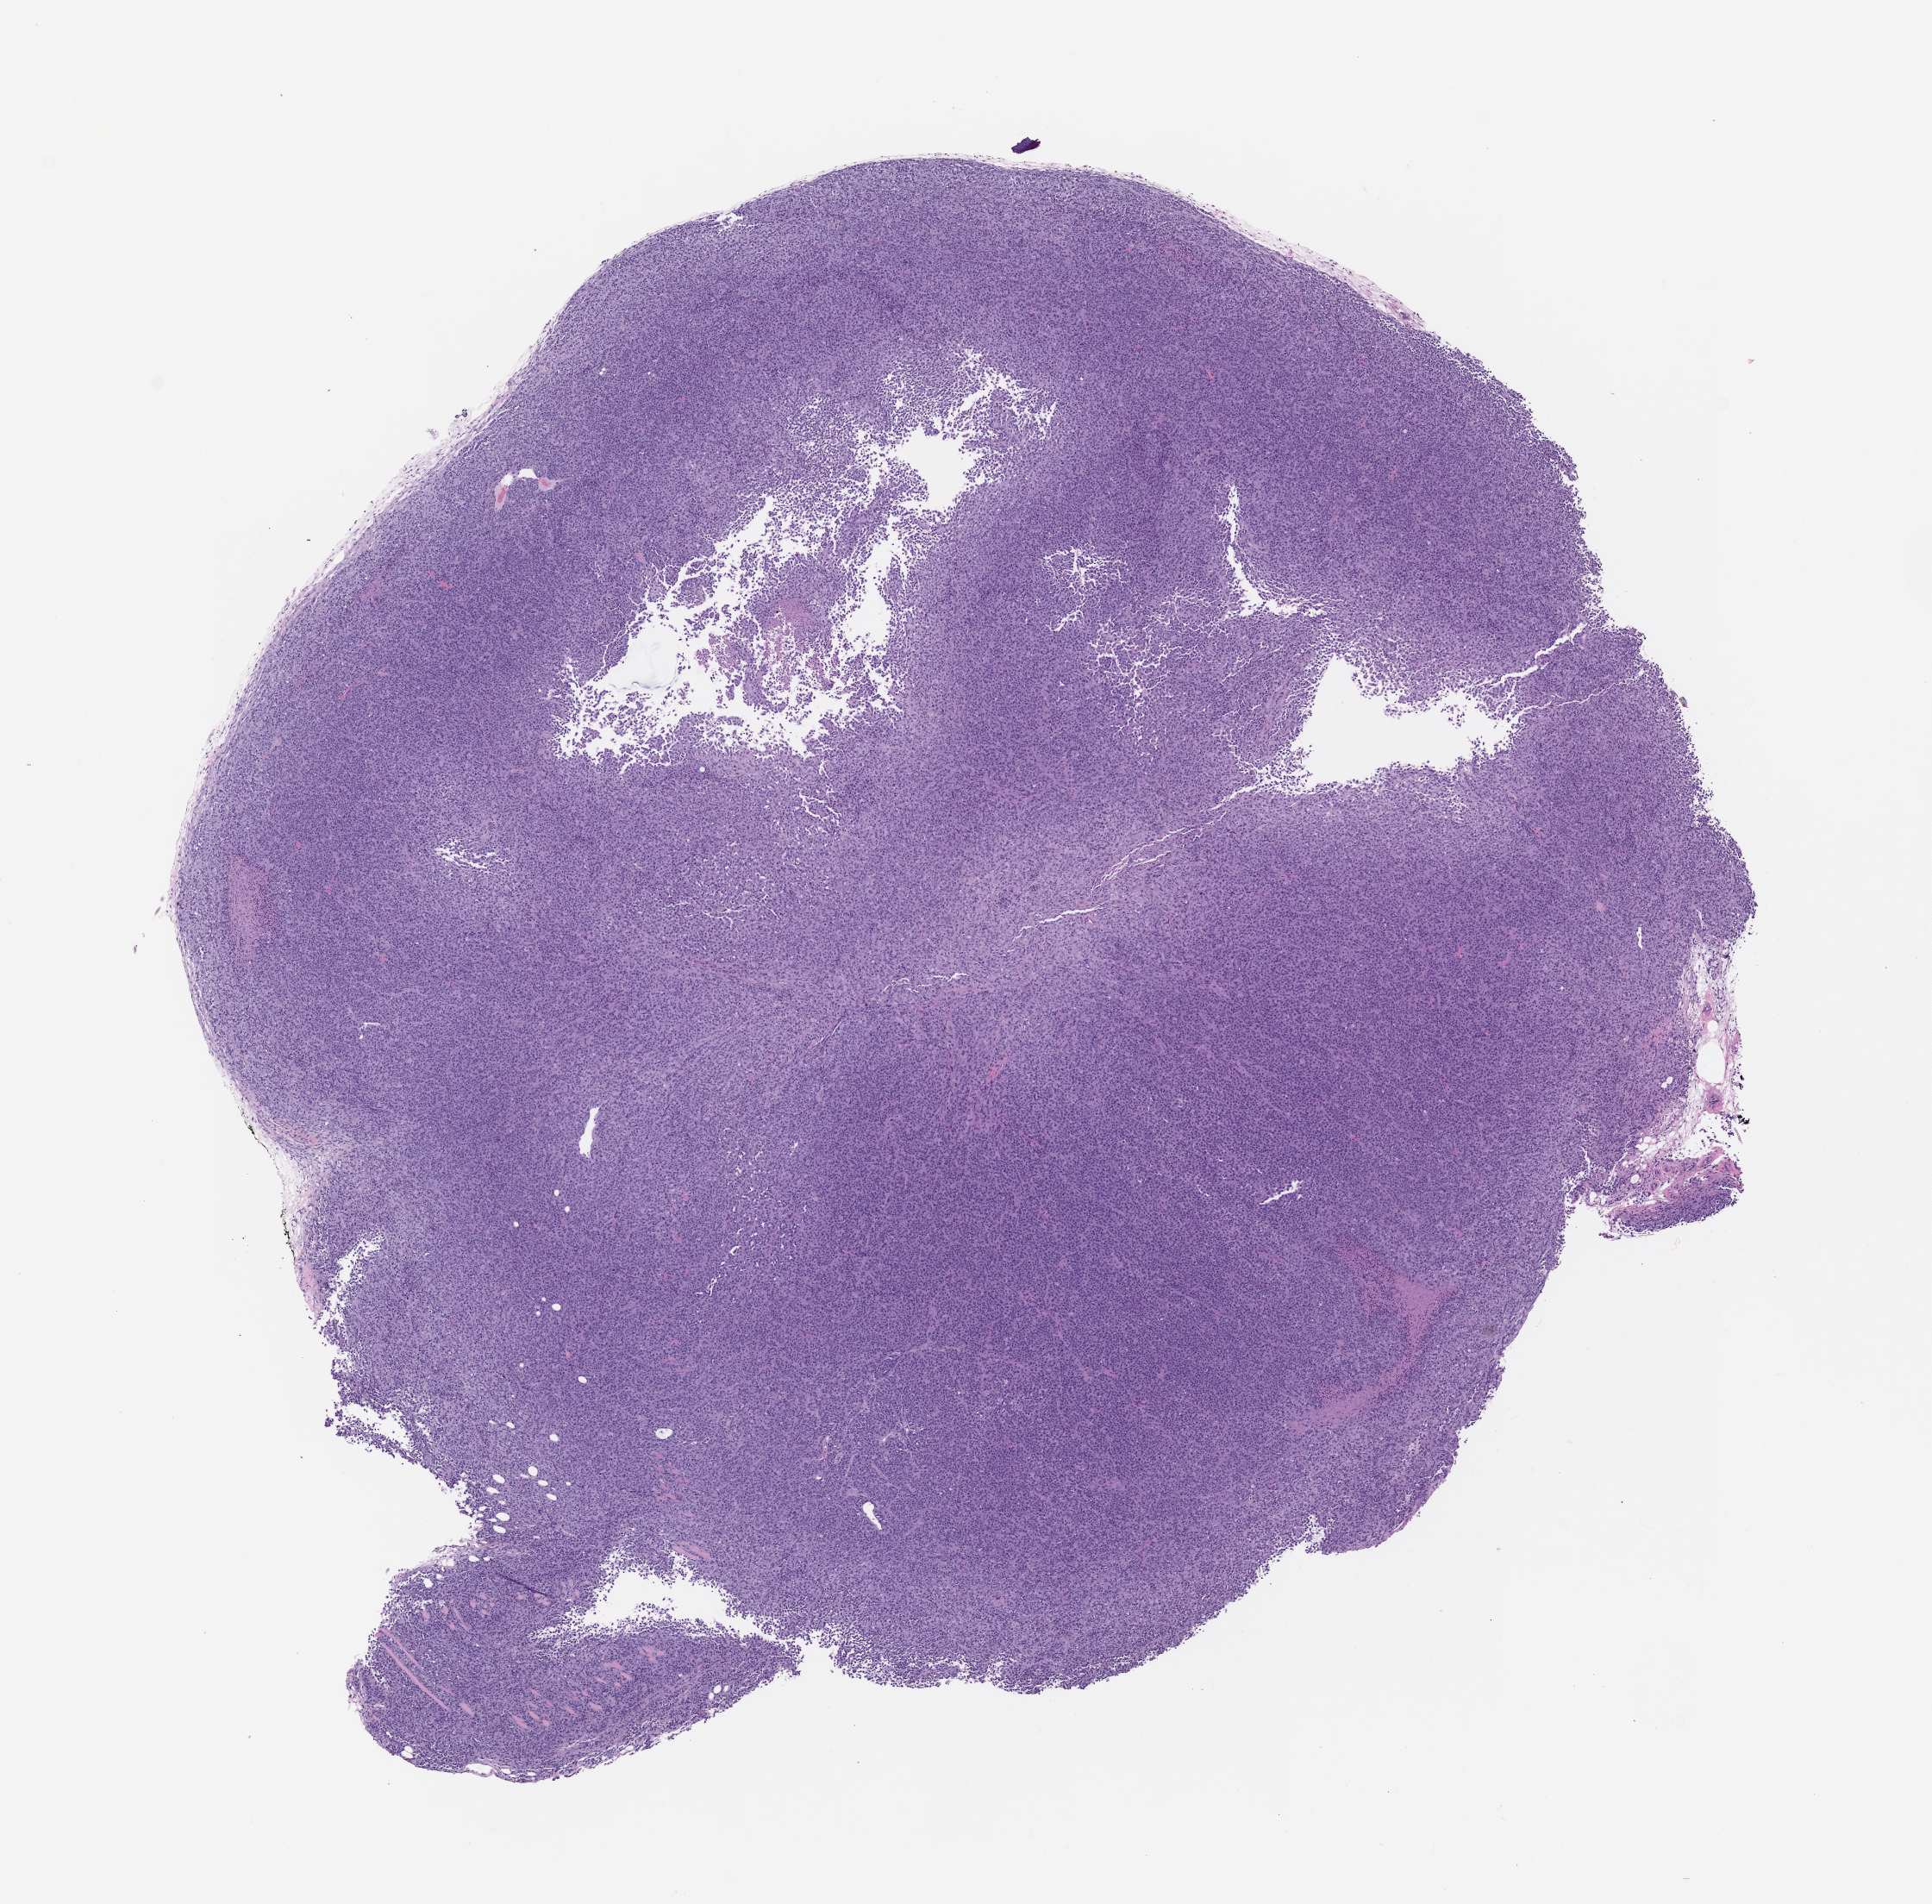
Whole-slide image, haematoxylin and eosin: patient-derived xenograft (human tumor grown in a mouse), passage 2 — shown as a low-resolution overview of the whole scanned area (about 9.0 x 8.9 mm). FFPE section.
Originating patient diagnosis: Mesothelial Neoplasm.